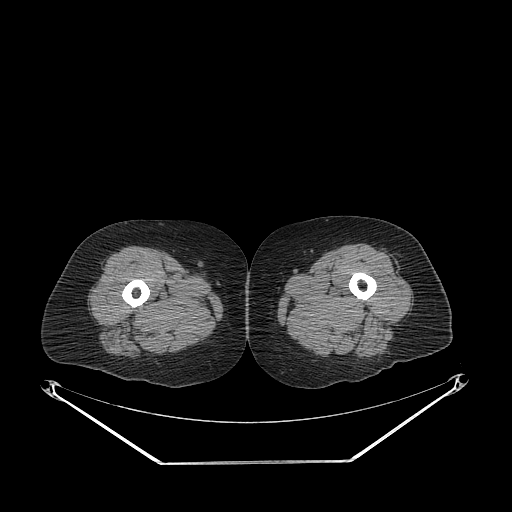
CT of an extremity soft-tissue mass (from a PET/CT study), one axial slice. Slice 247 of 311 in the series (ordered by position). Reconstruction kernel STANDARD. Soft-tissue window (W 400 / L 40 HU). 3.75 mm slice thickness. 512 × 512 image matrix, field of view 500 × 500 mm. Female patient. From the clinical record (not read from this slice): histological type: leiomyosarcoma; grade: intermediate; site of the primary tumour: parascapusular.
Outlined on this slice (expert contour drawn on MRI and transferred to this co-registered scan by the dataset authors):
- gross tumour volume including surrounding oedema: bounding box <201,270,211,279> (left, top, right, bottom; pixels)
- gross tumour volume (mass): <203,272,209,275>